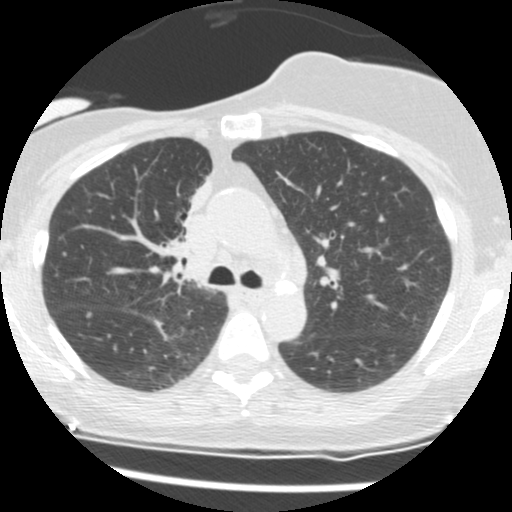
Chest CT (low-dose screening protocol), one axial image; second annual screen; lung window (W 1500 / L -600 HU); standard (soft-tissue) reconstruction kernel (STANDARD). Female, age 56 years at enrolment. Current smoker at enrolment.
• Expert-annotated lung lesion, bounding box <153,181,210,267> (left, top, right, bottom; pixels).
• The screening reader recorded 2 non-calcified nodules or masses ≥4 mm on this exam; which of them this box marks is not recorded.
• Participant outcome: lung cancer diagnosed 675 days after this screen — adenocarcinoma, NOS, right upper lobe, stage IIIB (AJCC 6th edition), 8 mm at pathology.